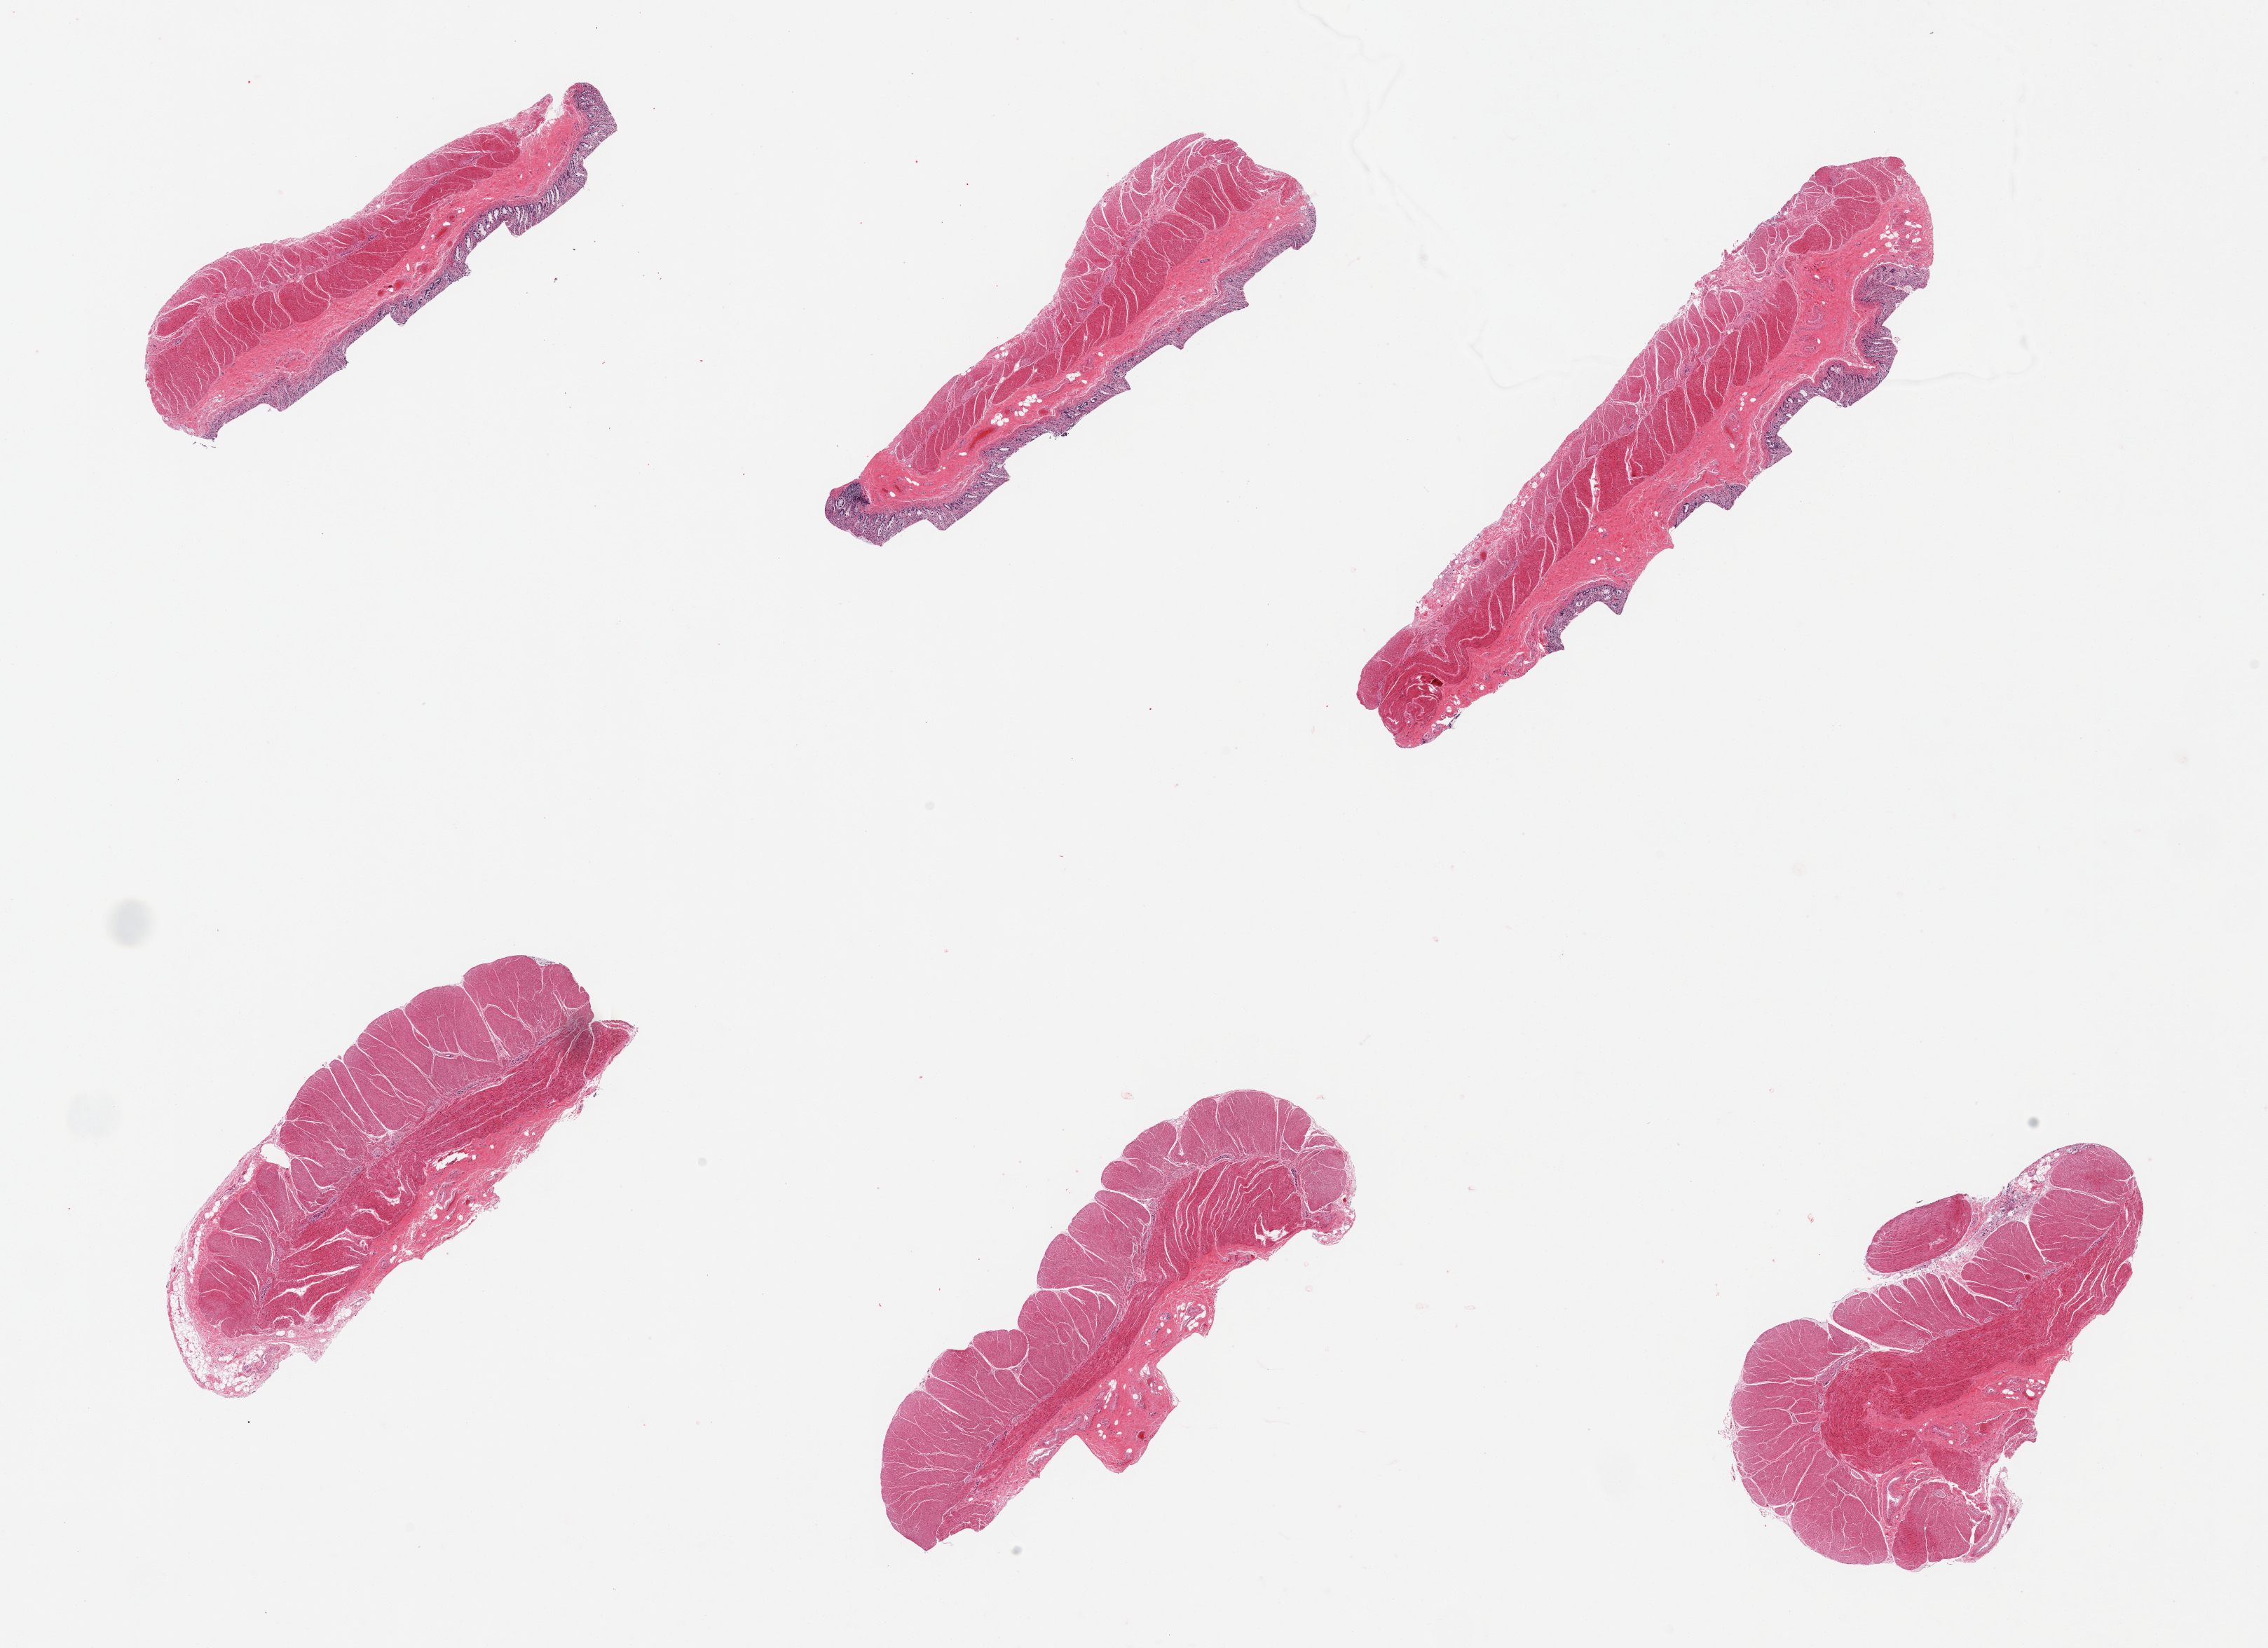
Digitized H&E-stained section — a low-resolution overview of the entire scanned area, about 25.6 x 18.6 mm; PAXgene-fixed, paraffin-embedded tissue; target tissue: sigmoid colon; donor tissue sample. Donor sex: female.
Reviewer comment on this tissue sample: 6 pieces; muscularis, 3 pieces include autolyzed mucosa (not target).